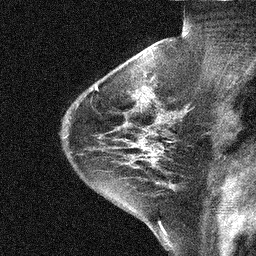
Breast MRI (dynamic contrast-enhanced), one sagittal slice; position 31 of 44 along the scan axis; dynamic contrast-enhanced study with each time point stored as its own series, time point 2 of 3 at this slice position (early post-contrast, ordered by acquisition time); 1.5 T; TE 5 ms, TR 10.3 ms; 3 mm slice thickness; 256 × 256 image matrix. Female patient, age 31 years. Case-level facts recorded for this patient, not image findings: setting: breast cancer imaged before/during neoadjuvant chemotherapy; receptor status: HER2-positive.
Structures marked on this image (semi-automatically segmented with operator editing):
- analysis volume of interest (the breast-tissue region the enhancement analysis was run in; not a lesion): box from (x=136, y=131) to (x=181, y=168) px
- tumour enhancement mask (voxels above the 90 % enhancement threshold inside the analysis volume of interest): (x=140, y=141)–(x=175, y=161)